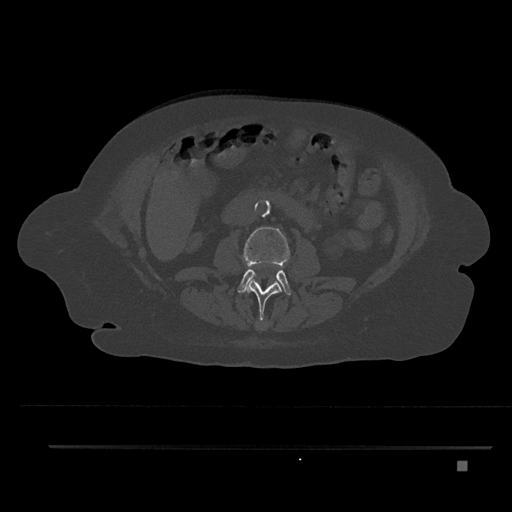
CT including the spine, one axial slice. Slice 152 of 797 in the series (ordered by position). Bone window (W 1800 / L 400 HU). 512 × 512 image matrix, field of view 437 × 437 mm. Female patient, age 76 years. From the clinical record (not read from this slice): primary cancer: lung; vertebrae with lytic lesions (as recorded): T11, L3.
Structures marked on this image (semi-automatically segmented with operator editing):
- L2 vertebra: bounding box (x1, y1, x2, y2) in pixels: (245, 280, 282, 327)
- L3 vertebra: (237, 227, 291, 295)